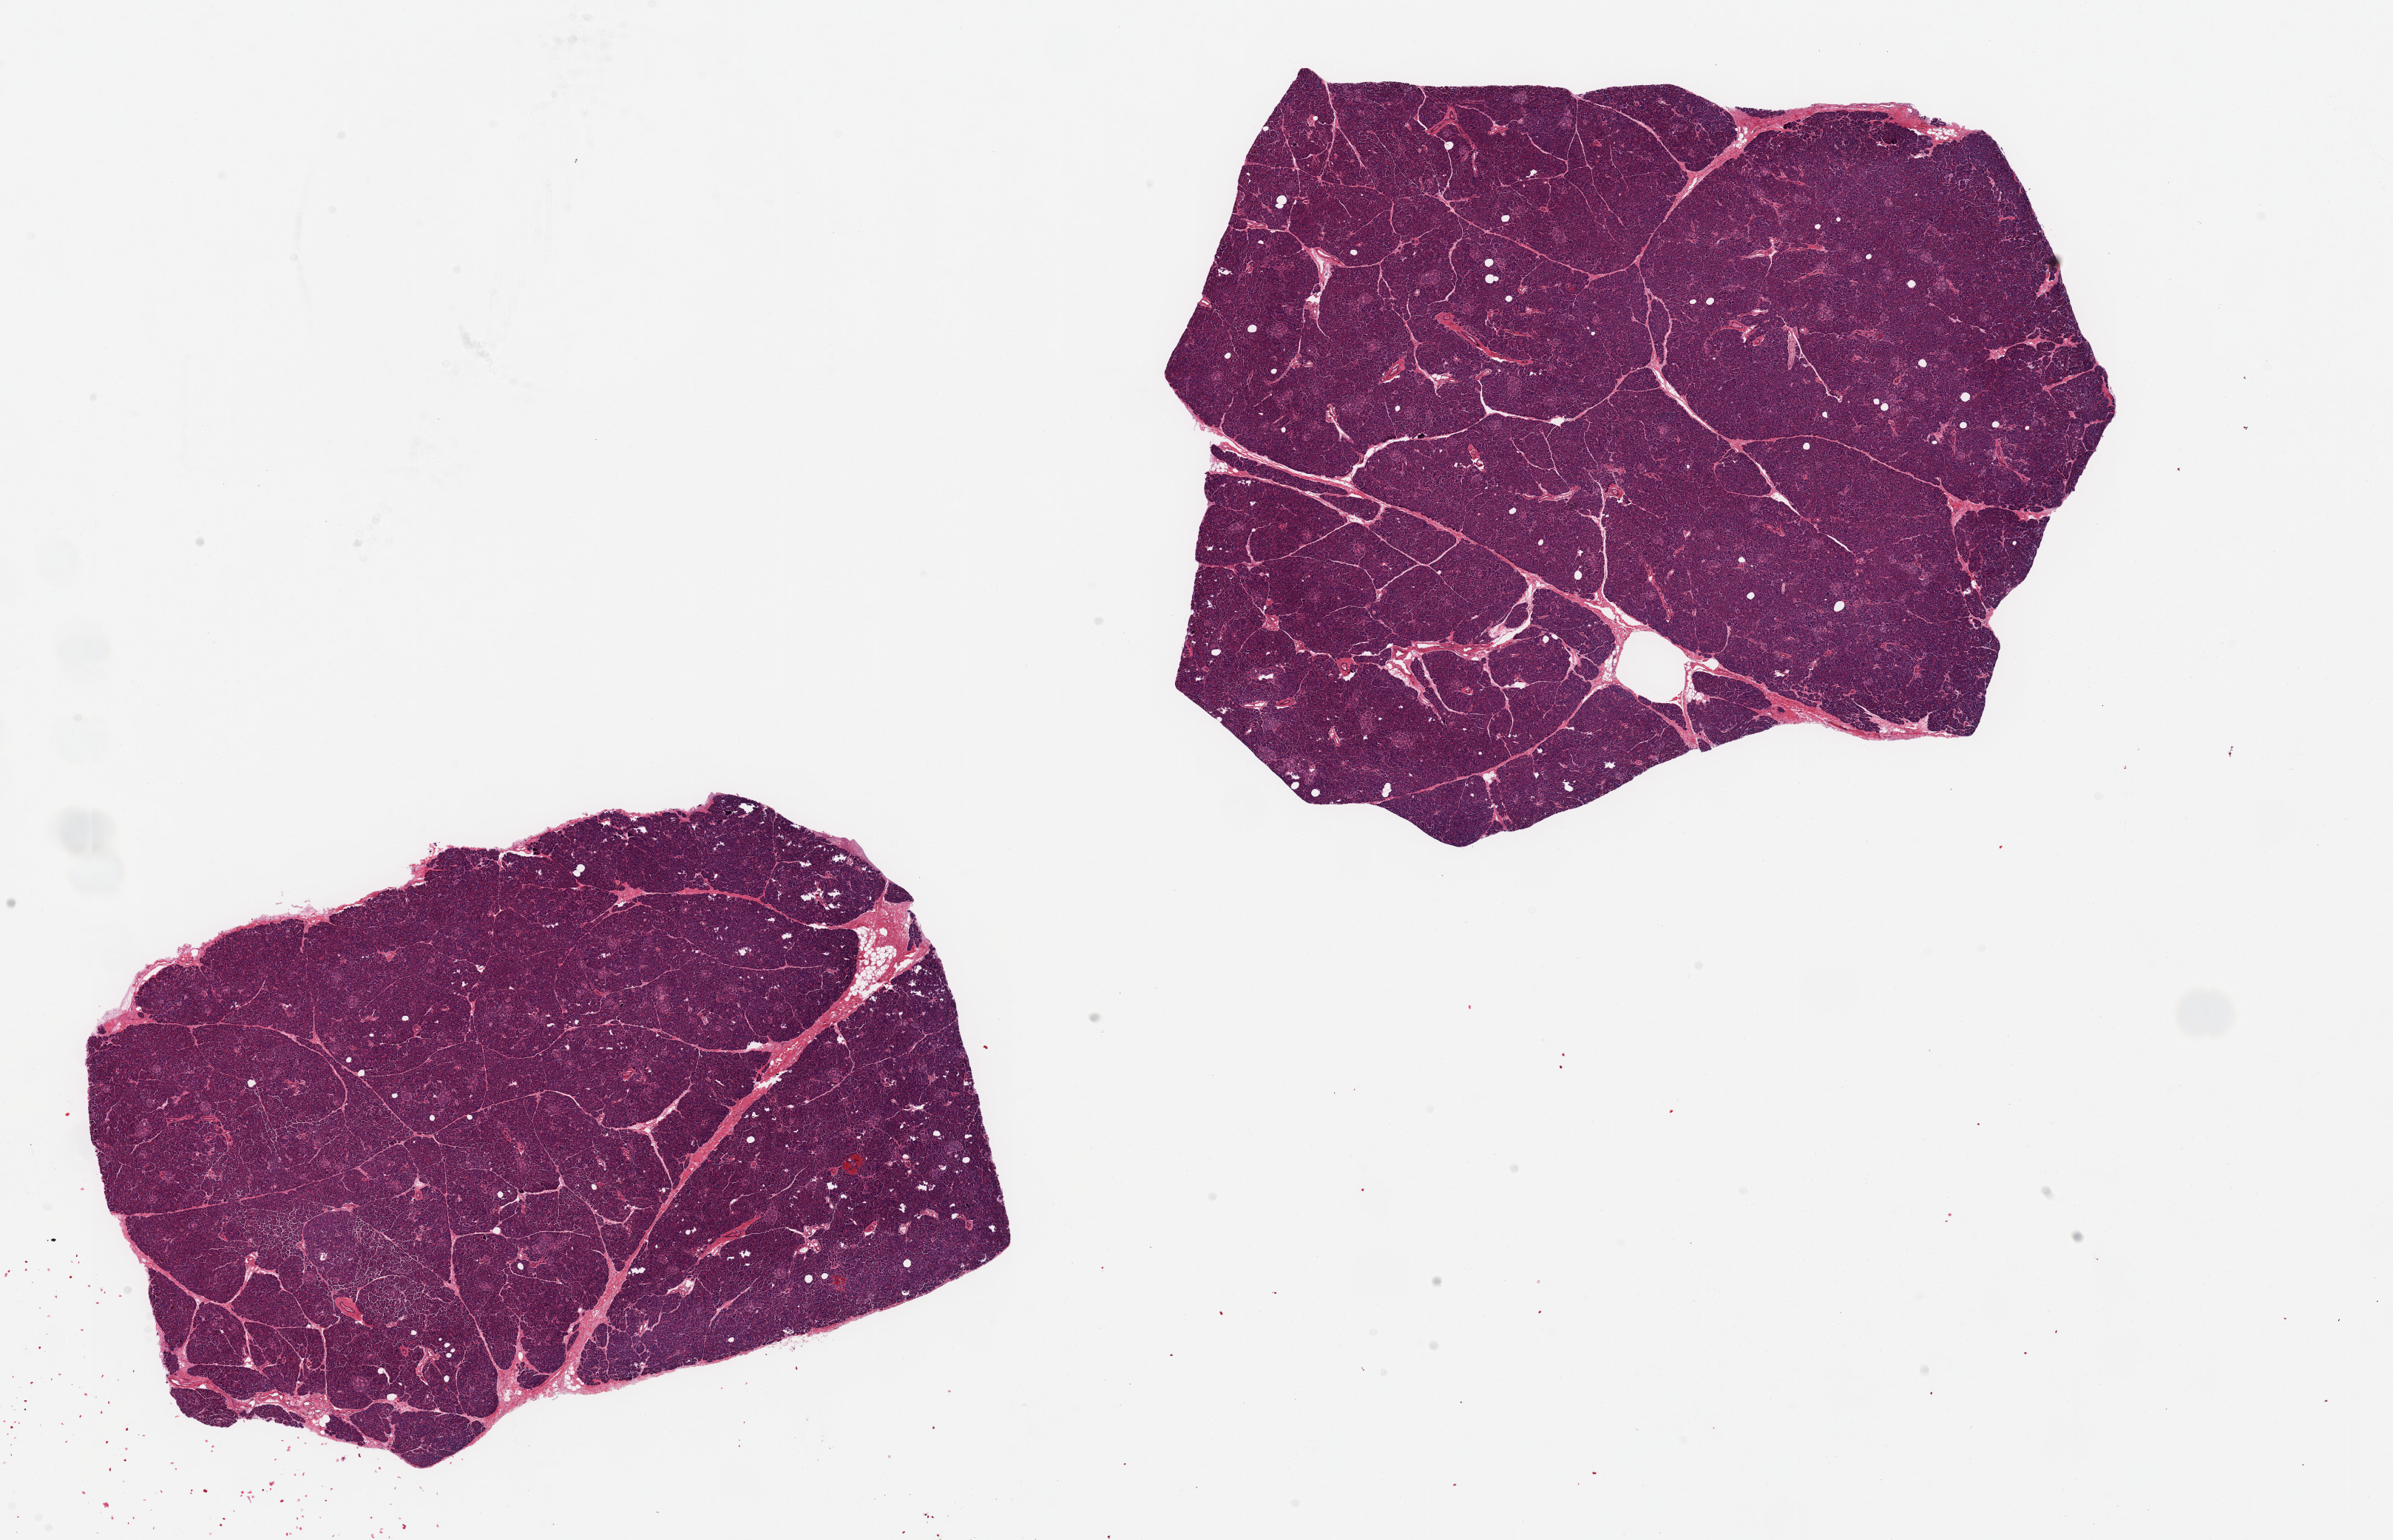
Whole-slide image, haematoxylin and eosin stain, a low-resolution overview of the entire scanned area, about 25.6 x 16.5 mm; PAXgene-fixed, paraffin-embedded tissue; sampled site (target tissue): pancreas; tissue donor sample. Donor: male.
Pathologist's review note for this sample: 2, ~ 10x8 mm pieces,<1% fat; focal fixation fractures.